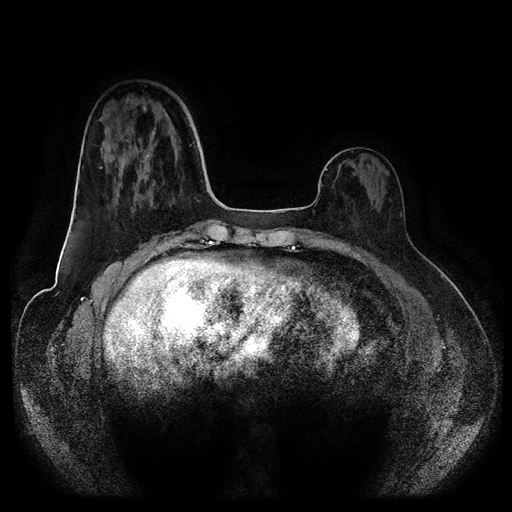
Breast MRI (dynamic contrast-enhanced, multi-phase), one axial slice. Slice 33 of 116 in the series (ordered by position). Dynamic contrast-enhanced series, time point 2 of 5 at this slice position (early post-contrast). 1.5 T. TE 2.6 ms, TR 5.2 ms. 2 mm slice thickness. 512 × 512 image matrix, field of view 380 × 380 mm. Female patient, age 50 years.
Structures marked on this image (semi-automatically segmented with operator editing):
- breast lesion (labelled benign in the annotation): bounding box [x1, y1, x2, y2] px = [136, 131, 156, 187]